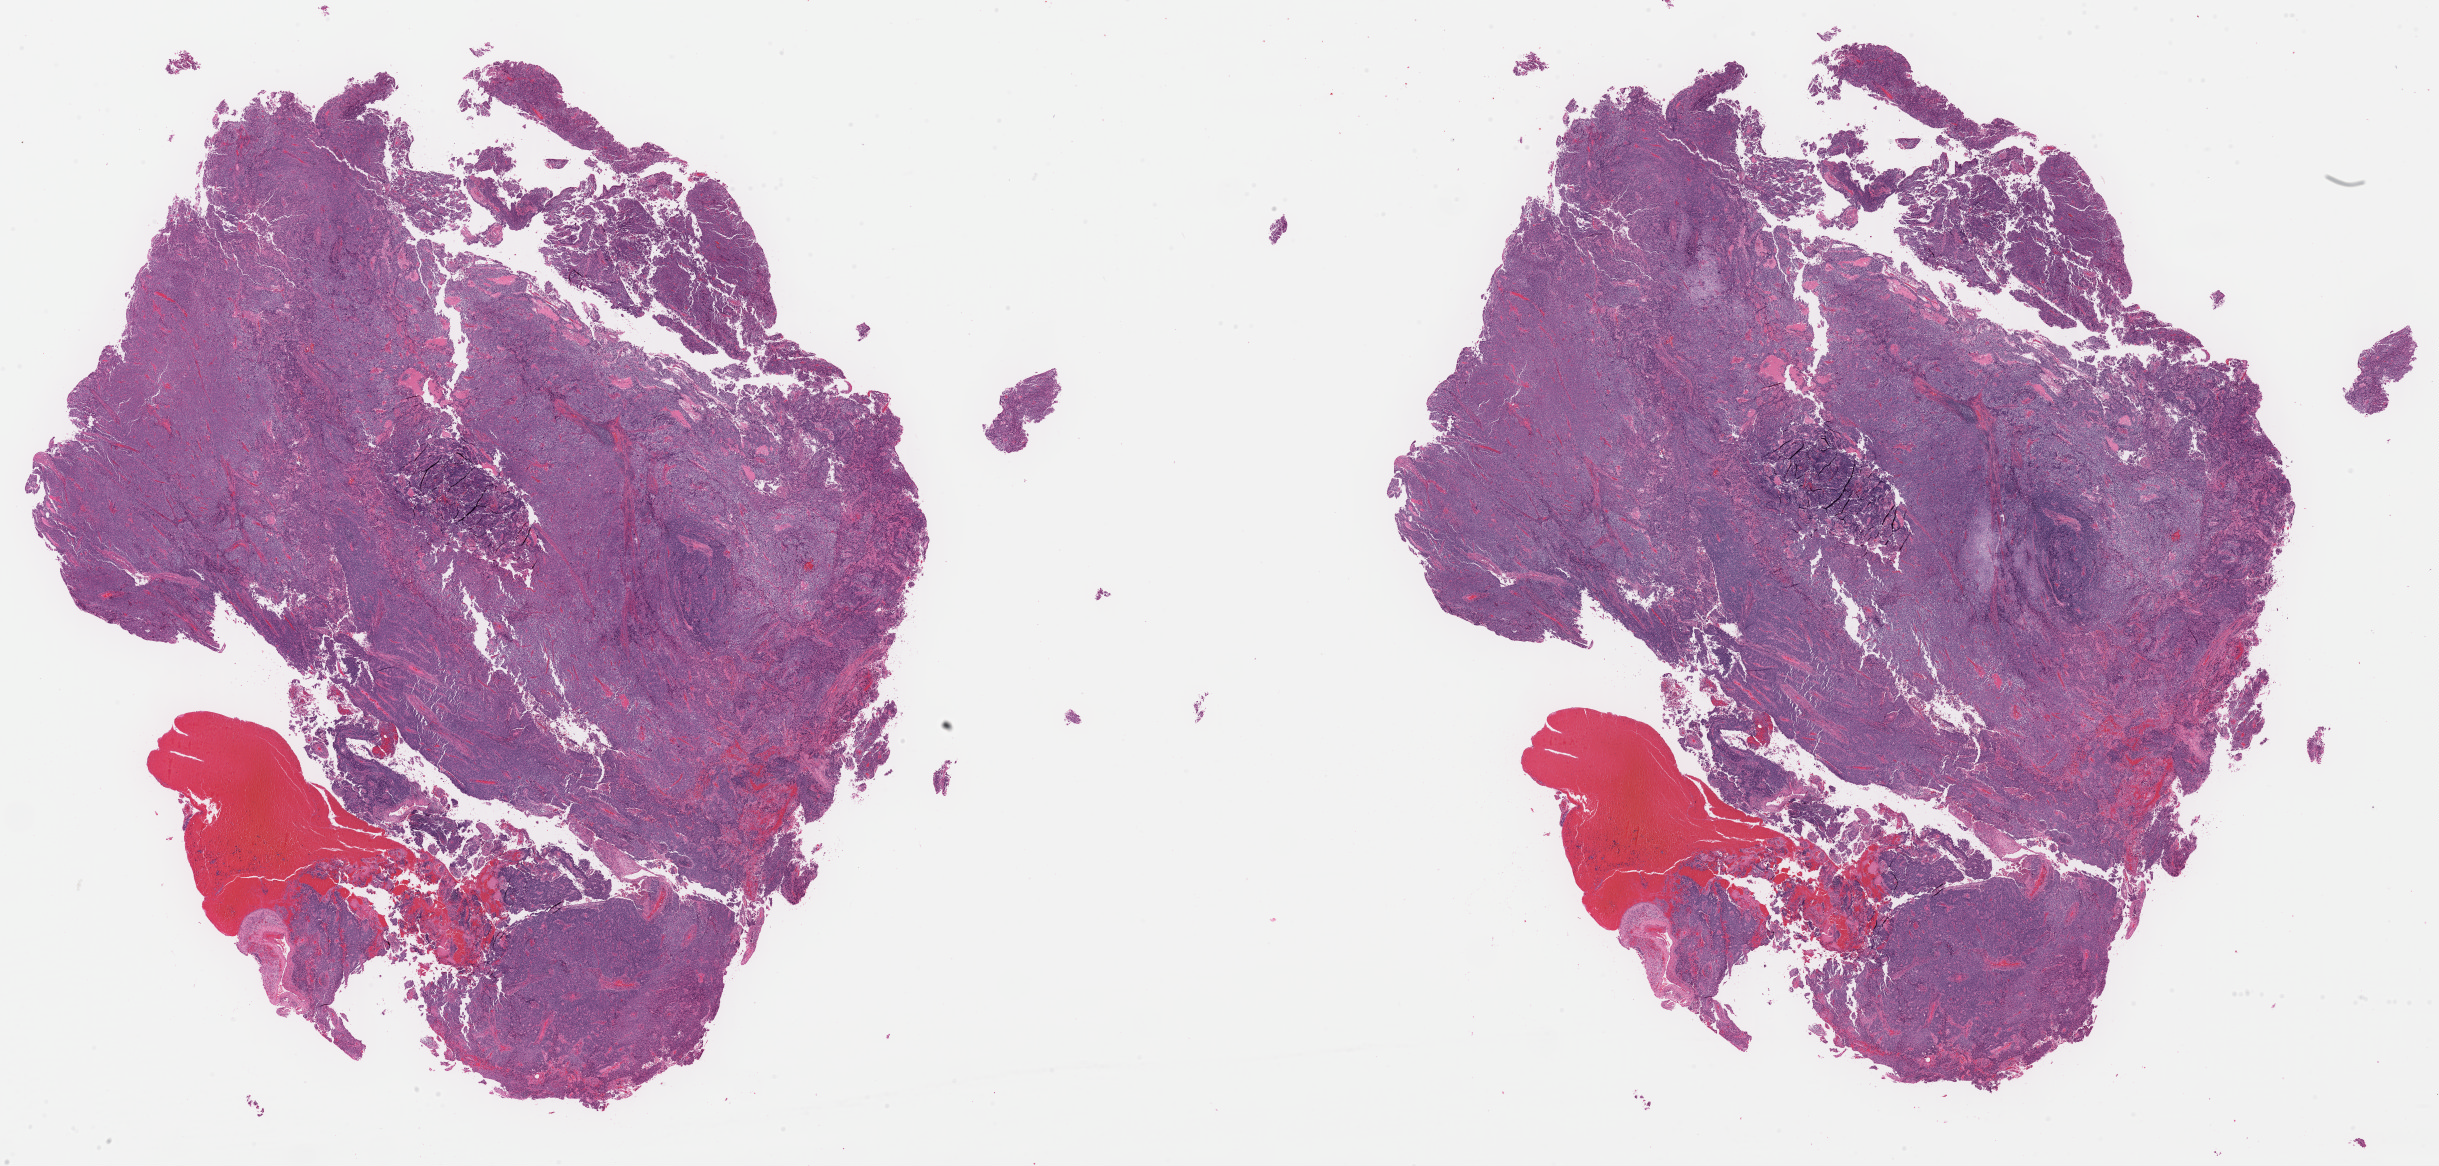
Whole-slide histology image, H&E, a low-resolution overview of the entire scanned area, about 38.5 x 18.4 mm, formalin-fixed paraffin-embedded (FFPE) diagnostic section, sample: primary tumour, uterus. Patient: female, age at initial diagnosis 67 years. Histologic grade: G3 (poorly differentiated).
Lymph nodes positive (case pathology): 0 of 9 examined. Histologic diagnosis: Endometrioid adenocarcinoma, NOS (endometrium). FIGO stage: IA.